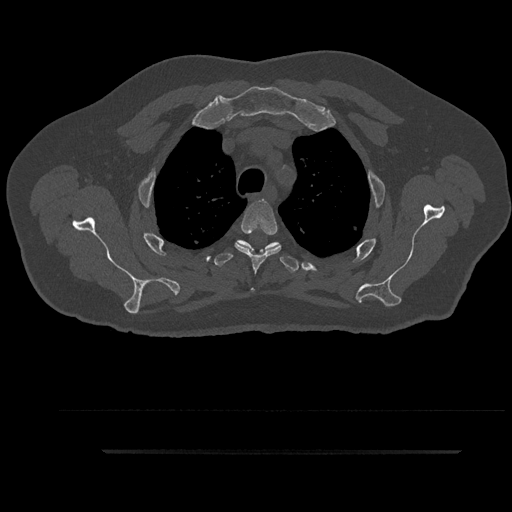
CT including the spine, one axial slice; position 705 of 797 along the scan axis; reconstruction kernel Br40s/3; 120 kVp; bone window (W 1800 / L 400 HU); 0.5 mm slice thickness; 512 × 512 image matrix, field of view 432 × 432 mm. Male patient, age 63 years. From the clinical record (not read from this slice): primary cancer: renal; vertebrae with lytic lesions (as recorded): T8.
Structures marked on this image (semi-automatically segmented with operator editing):
- T3 vertebra: bounding box (x1, y1, x2, y2) in pixels: (235, 200, 281, 272)
- T4 vertebra: (214, 240, 299, 273)